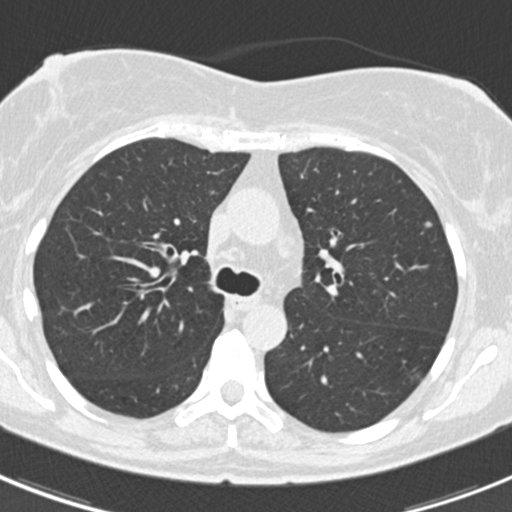
Chest CT (low-dose screening protocol), one axial image. Baseline annual screen. Lung window (W 1500 / L -600 HU). 120 kVp. Slice 72 of 184 in the series. Female, age 60 years at enrolment.
Expert reader's lesion annotation, bounding box [x1, y1, x2, y2] px = [415, 215, 442, 241]. The screening reader recorded 3 non-calcified nodules or masses ≥4 mm on this exam (lingula, left lower lobe, lingula); which of them this box marks is not recorded. Official screen result: positive, change unspecified: nodule(s) >= 4 mm or enlarging nodule(s), mass(es), or other non-specific abnormalities suspicious for lung cancer. Later outcome: lung cancer diagnosed 886 days after this screen — non-small cell carcinoma, left upper lobe, poorly differentiated (G3), stage IB (AJCC 6th edition), 7 mm at pathology.